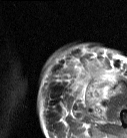
MRI of an extremity soft-tissue mass, one axial slice; position 17 of 87 along the scan axis; T2-weighted fat-saturated; MR volume resampled by the dataset authors to the PET/CT grid (not the native acquisition matrix); 3.27 mm slice thickness; 127 × 138 image matrix, field of view 124 × 135 mm. Female patient. Case-level facts recorded for this patient, not image findings: histological type: pleiomorphic leiomyosarcoma; grade: high; site of the primary tumour: left biceps.
Outlined on this slice (expert contour drawn on MRI and transferred to this co-registered scan by the dataset authors):
- gross tumour volume including surrounding oedema: bounding box <63,62,119,104> (left, top, right, bottom; pixels)
- gross tumour volume (mass): <63,62,114,86>